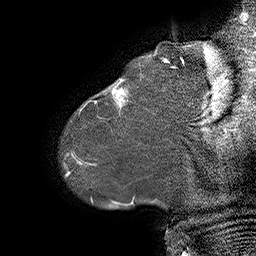
Breast MRI (dynamic contrast-enhanced), one sagittal slice. Dynamic contrast-enhanced series, time point 2 of 6 at this slice position (early post-contrast). 1.5 T. TE 4.5 ms, TR 32.4 ms. 3 mm slice thickness. 256 × 256 image matrix, field of view 180 × 180 mm. Female patient. From the clinical record (not read from this slice): setting: breast cancer imaged before/during neoadjuvant chemotherapy; receptor status: HER2-positive.
Structures marked on this image (semi-automatically segmented with operator editing):
- analysis volume of interest (the breast-tissue region the enhancement analysis was run in; not a lesion): bounding box [x1, y1, x2, y2] px = [80, 64, 163, 134]
- tumour enhancement mask (voxels above the 100 % enhancement threshold inside the analysis volume of interest): [111, 79, 127, 107]